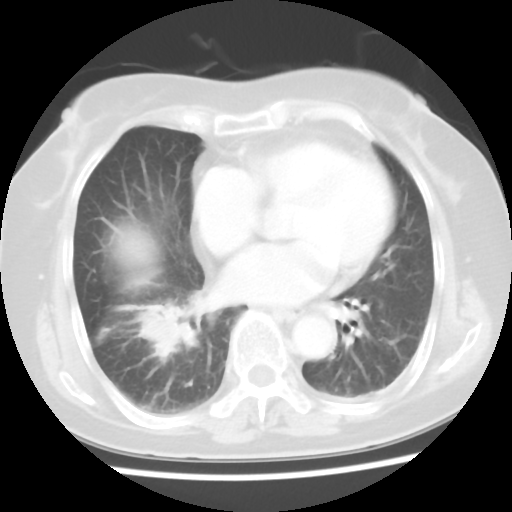
Chest CT, one axial slice; slice 17 of 45 in the series (ordered by position); reconstruction kernel STANDARD; 120 kVp; lung window (W 1500 / L -600 HU); 5 mm slice thickness; 512 × 512 image matrix. Female patient, age 65 years. Case-level facts recorded for this patient, not image findings: clinical TNM (as recorded): T2 N3 M0.
Structures marked on this image (rectangle marked by the reading radiologist):
- lung tumour (recorded histology: adenocarcinoma): box from (x=128, y=303) to (x=199, y=374) px